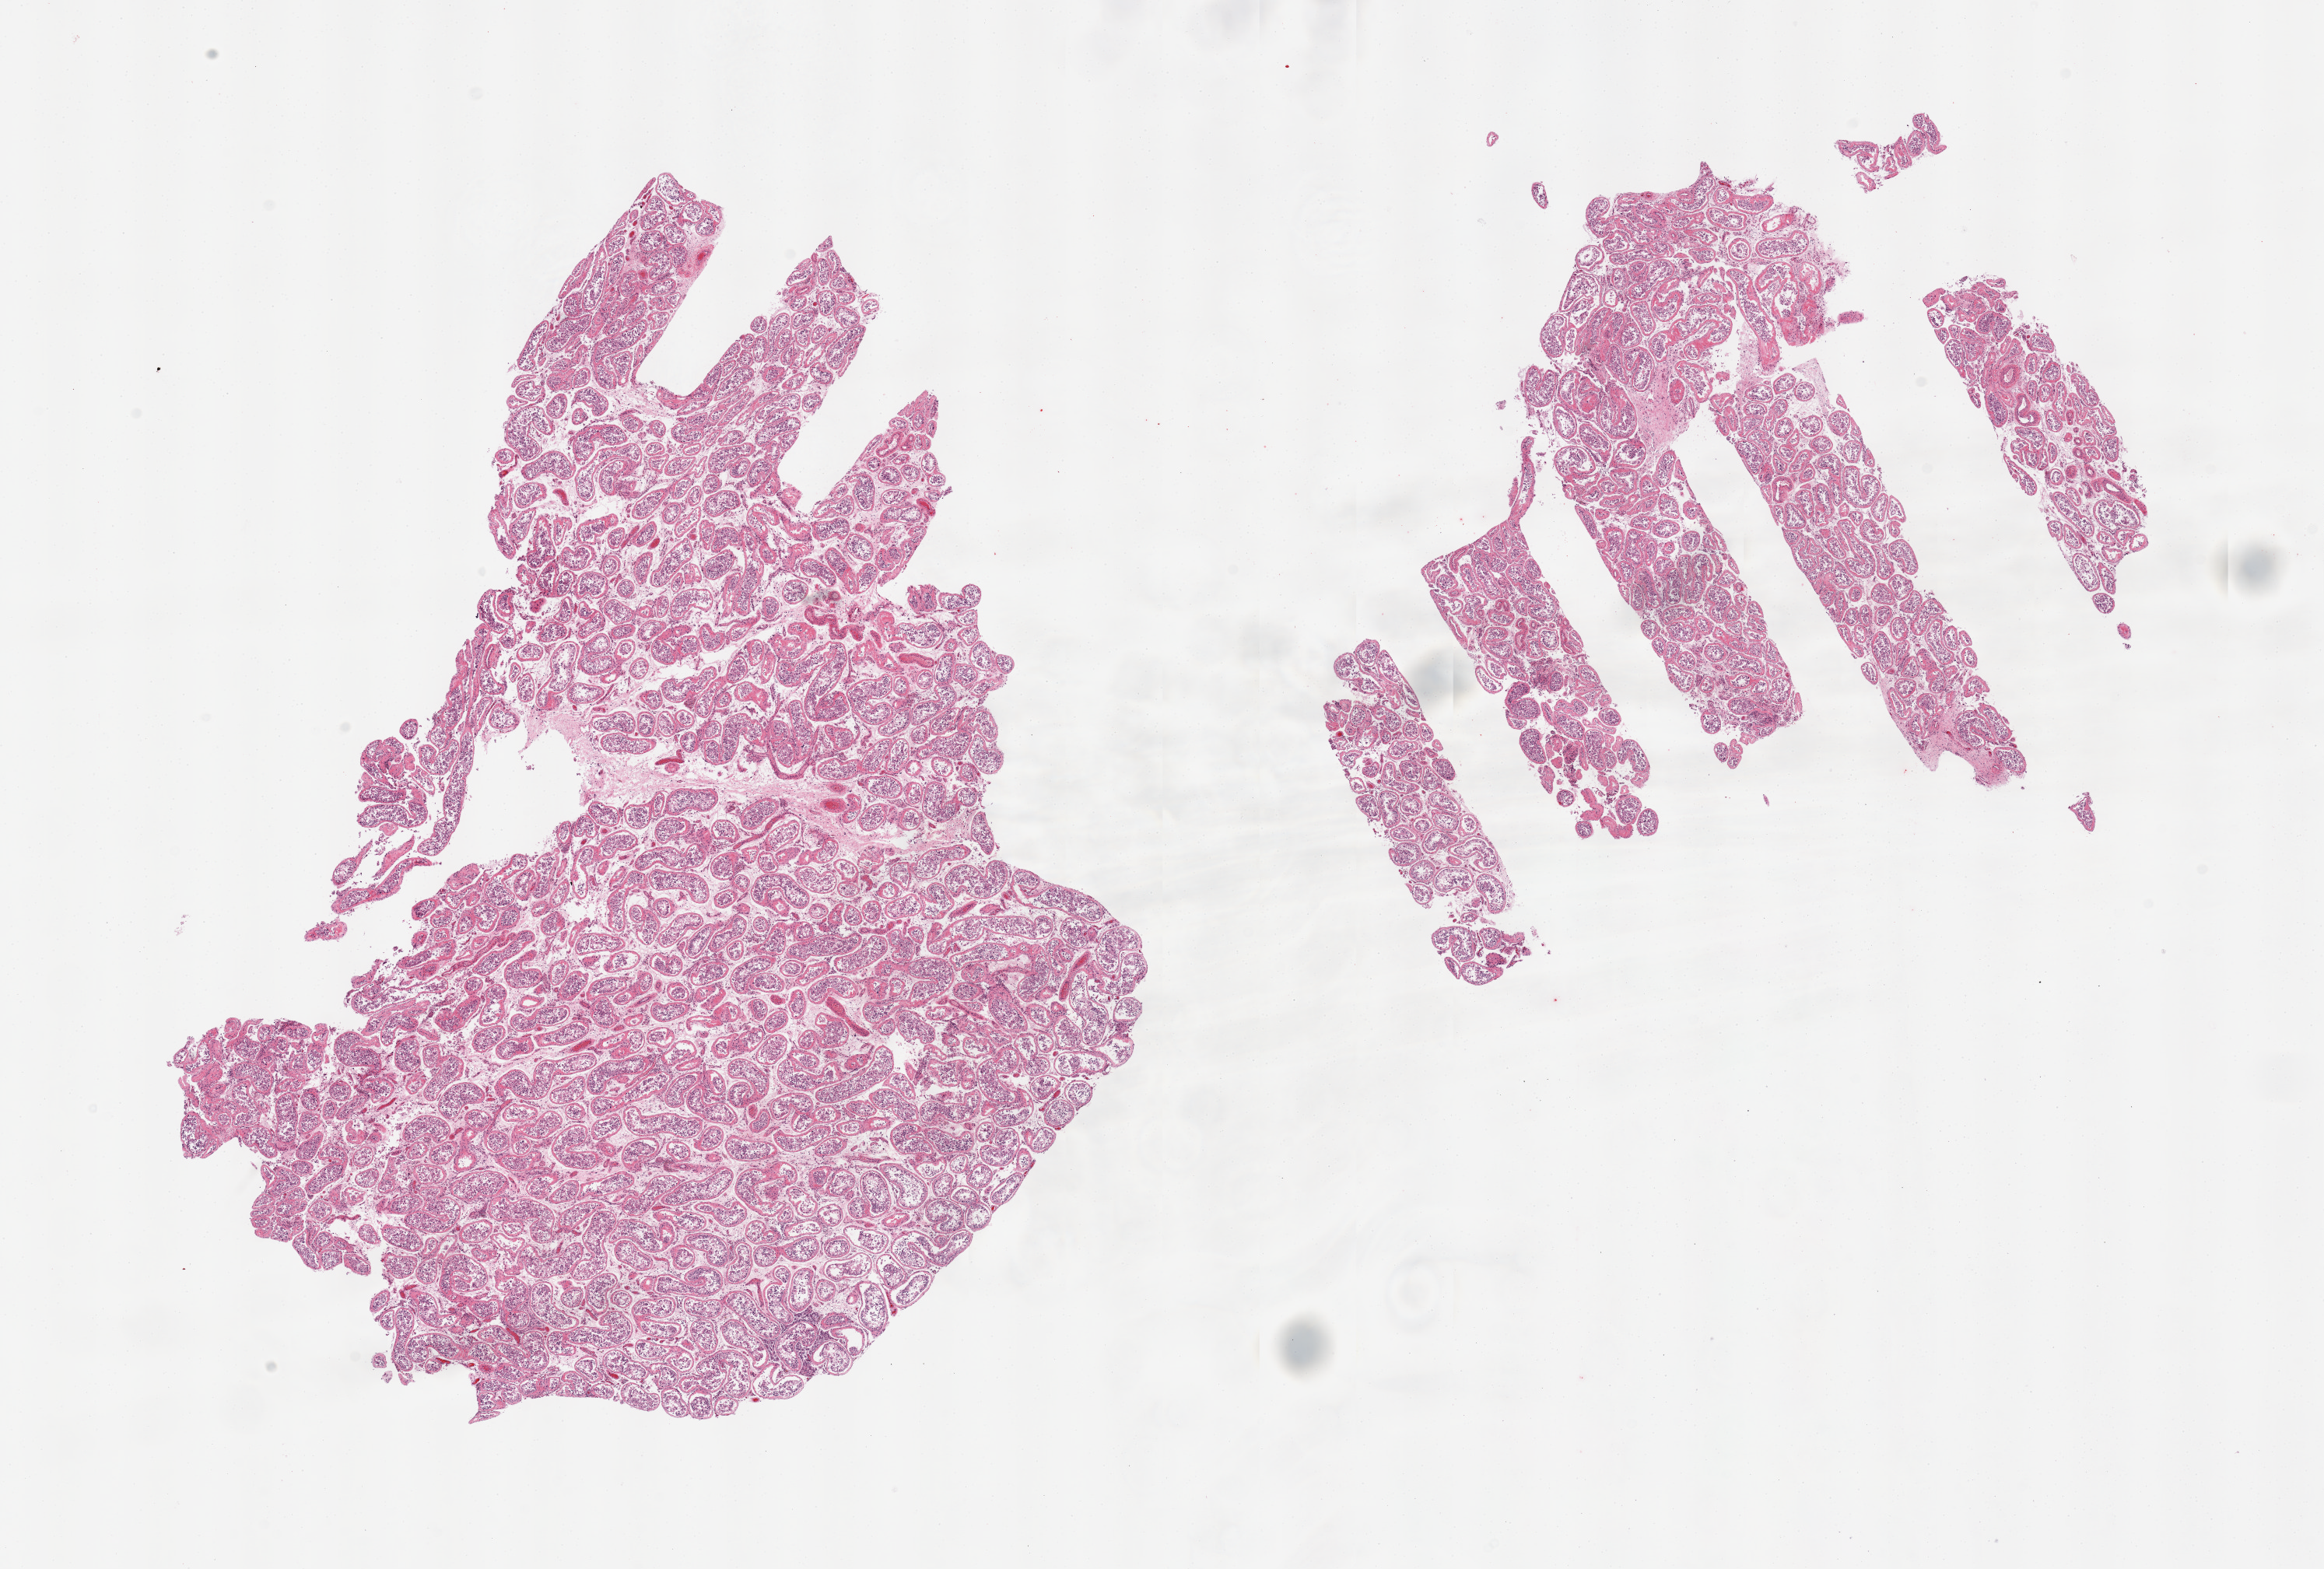
Digitized haematoxylin and eosin-stained section — low-resolution overview of the scanned area, about 23.6 x 16.0 mm. PAXgene-fixed, paraffin-embedded tissue. Section of testis (target tissue). Donor tissue sample. Donor: male.
- reviewer comment on this tissue sample: 2 pieces; decreased spermatogenesis